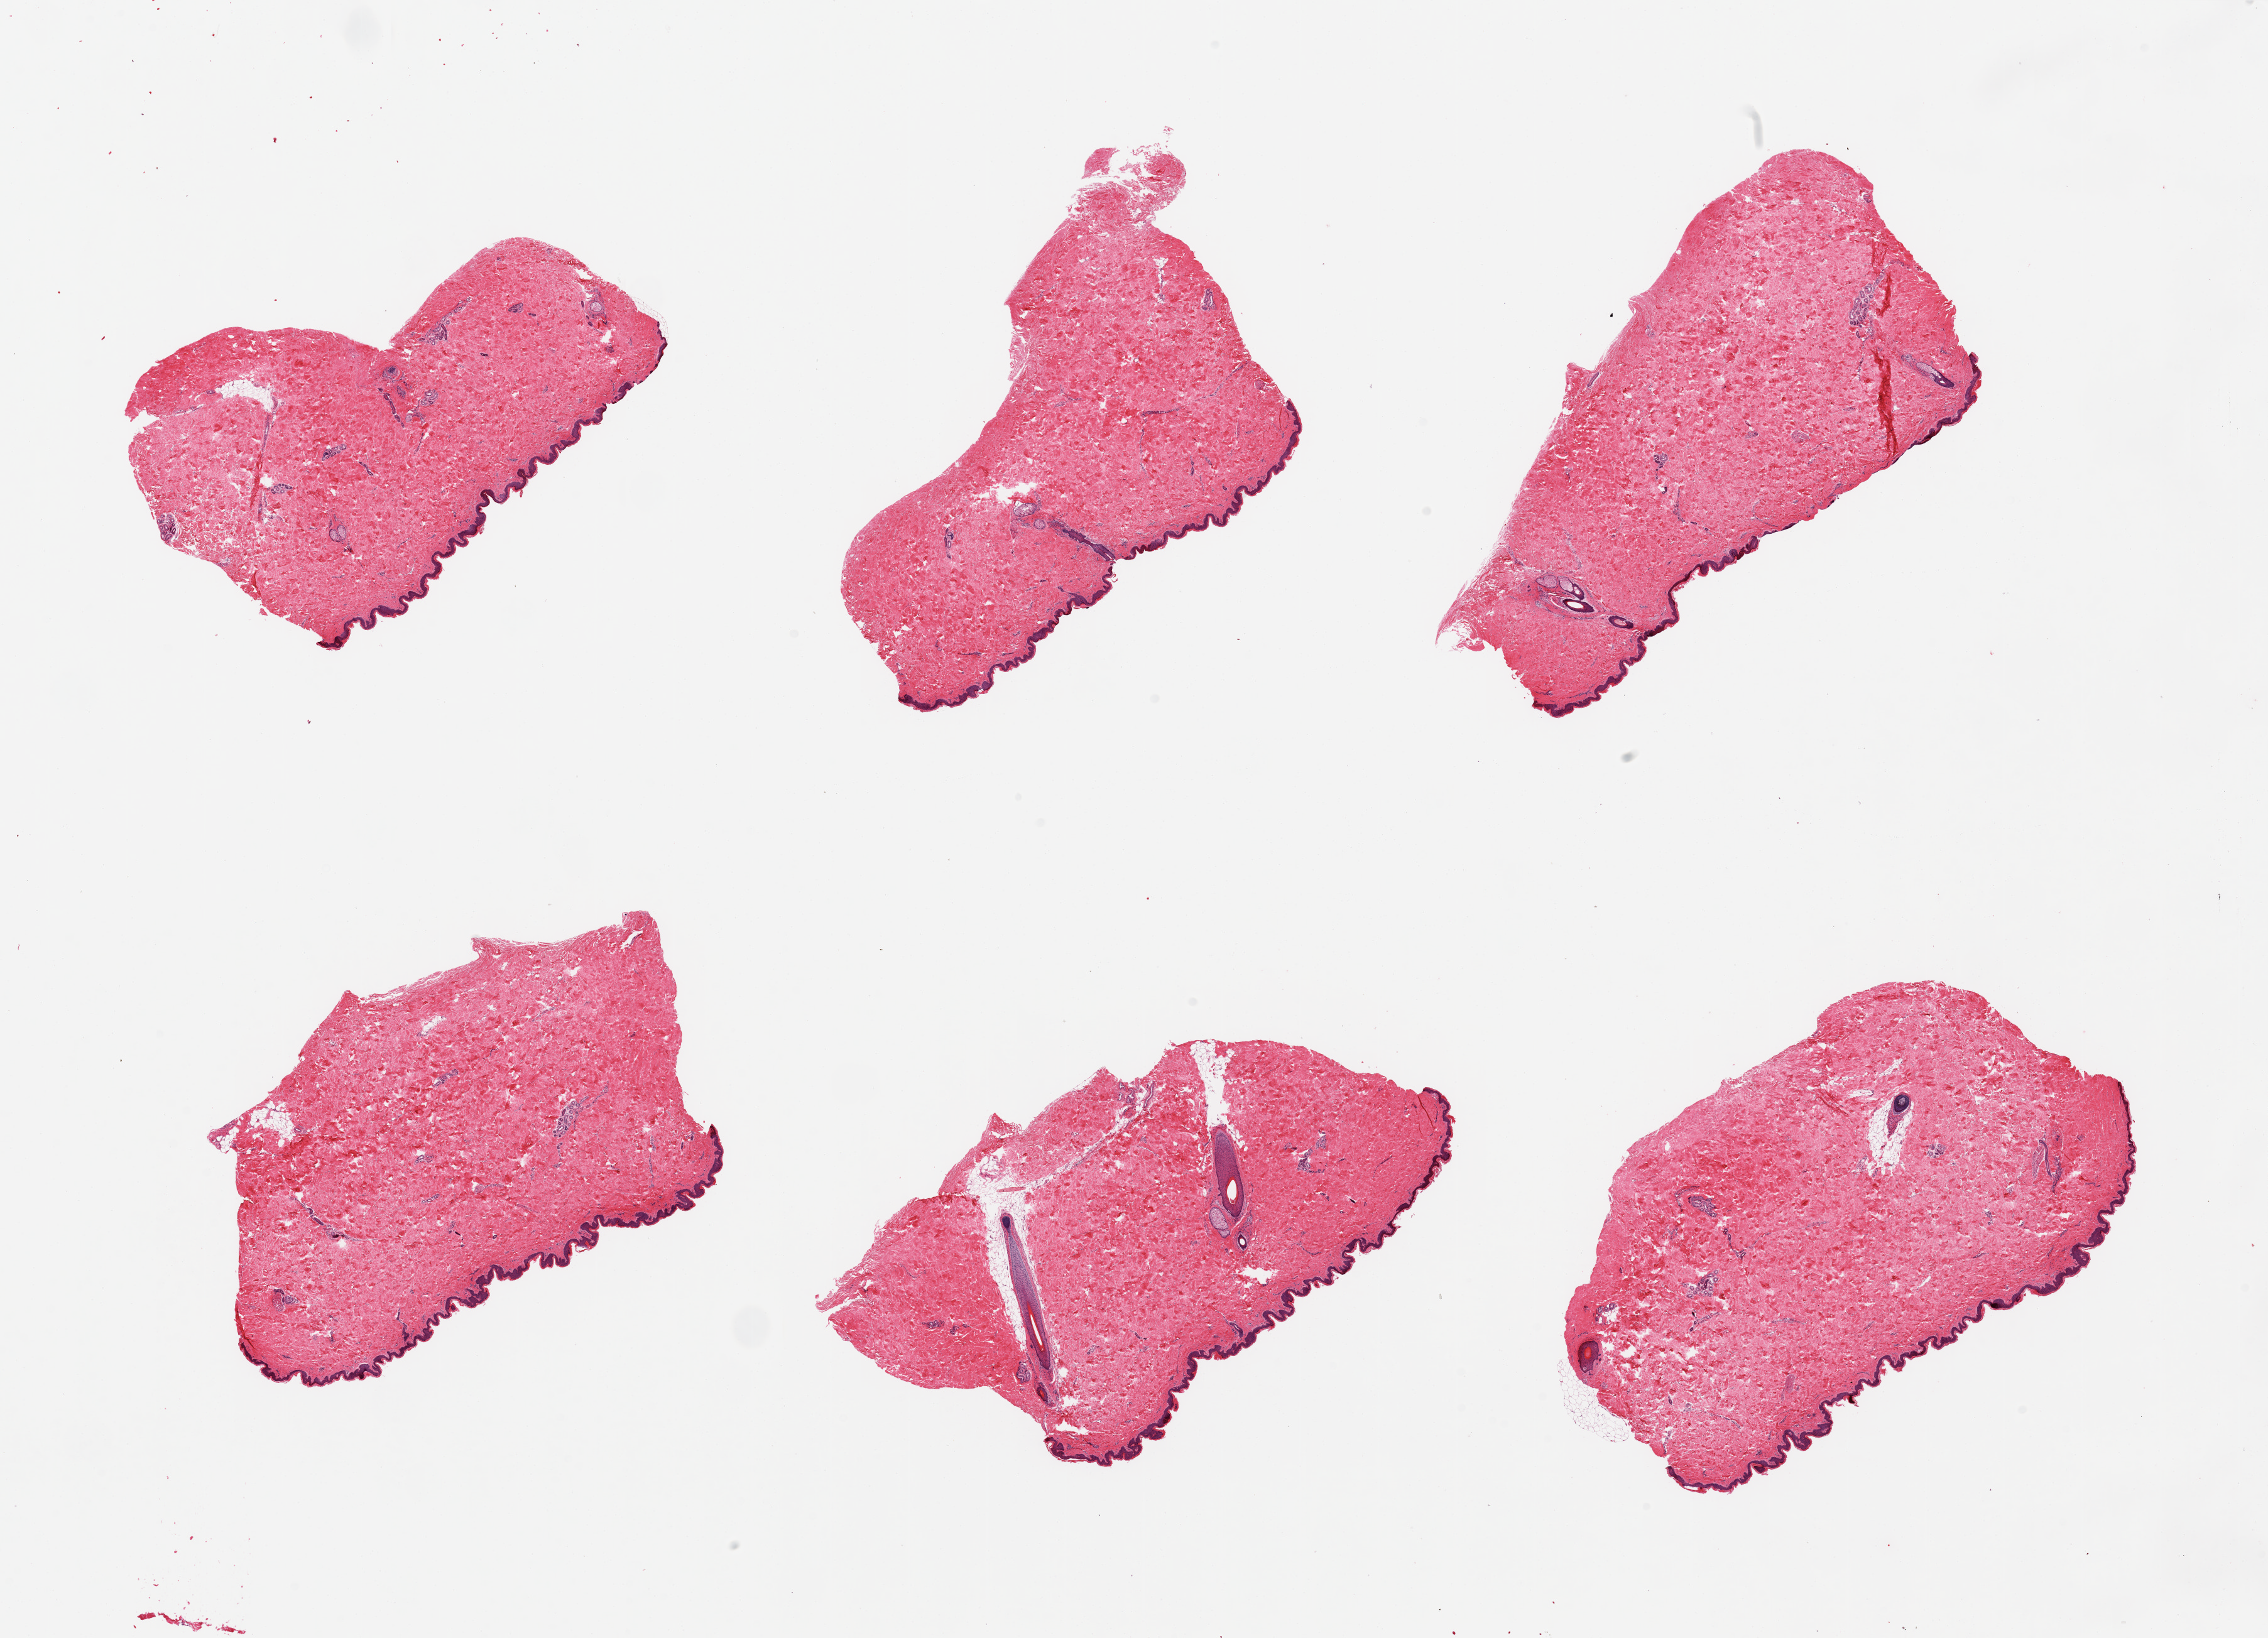
Whole-slide image, haematoxylin and eosin stain, brightfield, shown as a low-resolution overview of the whole scanned area (about 28.5 x 20.6 mm, acquisition: 20x scan); PAXgene-fixed paraffin-embedded (PFPE) section; sampled site (target tissue): skin of suprapubic region; donor tissue sample. Donor: male.
* review note (as recorded): 6 pieces, no dermal fat; squamous epithelium is ~ 40-50 microns